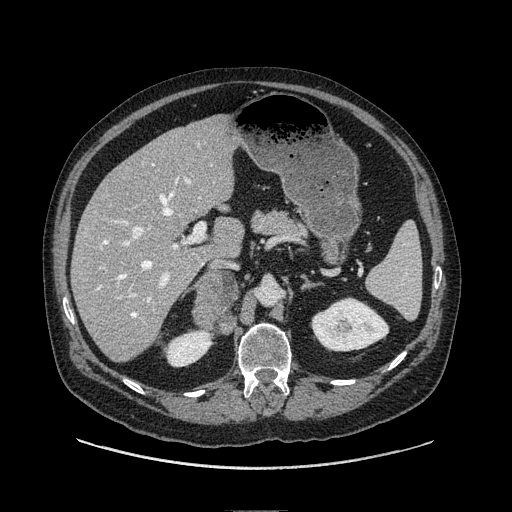
Contrast-enhanced abdominal CT, one axial slice. Position 51 of 149 along the scan axis. Soft-tissue window (W 400 / L 40 HU). 1.25 mm slice thickness. 512 × 512 image matrix, field of view 440 × 440 mm. Male patient. Case-level facts recorded for this patient, not image findings: diagnosis: adrenocortical carcinoma; tumour side: right adrenal; tumour size at pathology: 7.5 cm.
Structures marked on this image (semi-automatically segmented with operator editing):
- mass: bounding box (x1, y1, x2, y2) in pixels: (193, 271, 237, 325)